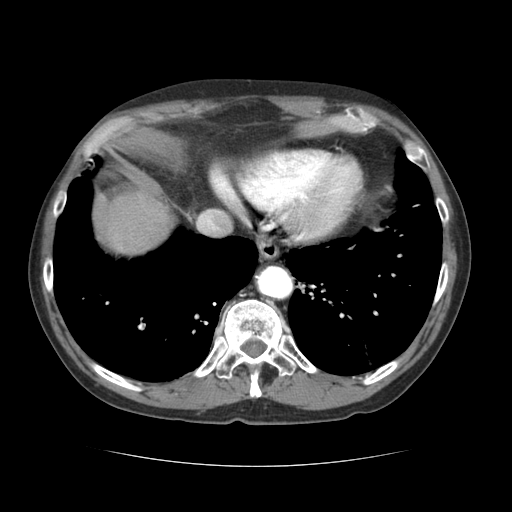
Contrast-enhanced abdominal CT (liver protocol), one axial slice. Slice 59 of 69 in the series (ordered by position). Soft-tissue window (W 400 / L 40 HU). 2.5 mm slice thickness. 512 × 512 image matrix, field of view 360 × 360 mm. Case-level facts recorded for this patient, not image findings: diagnosis: hepatocellular carcinoma (patient treated with transarterial chemoembolisation; whether this scan precedes or follows treatment is not stated here); TNM stage (as recorded): Stage-II; Child-Pugh class: B; tumour differentiation: poorly differentiated; tumour nodularity: multinodular.
Annotated regions visible in this slice (semi-automatic segmentation, software-assisted and operator-edited):
- liver parenchyma outside the tumour (the mass and vessels are separate outlines, so this box may not span the whole liver): bounding box (x1, y1, x2, y2) in pixels: (98, 192, 174, 254)